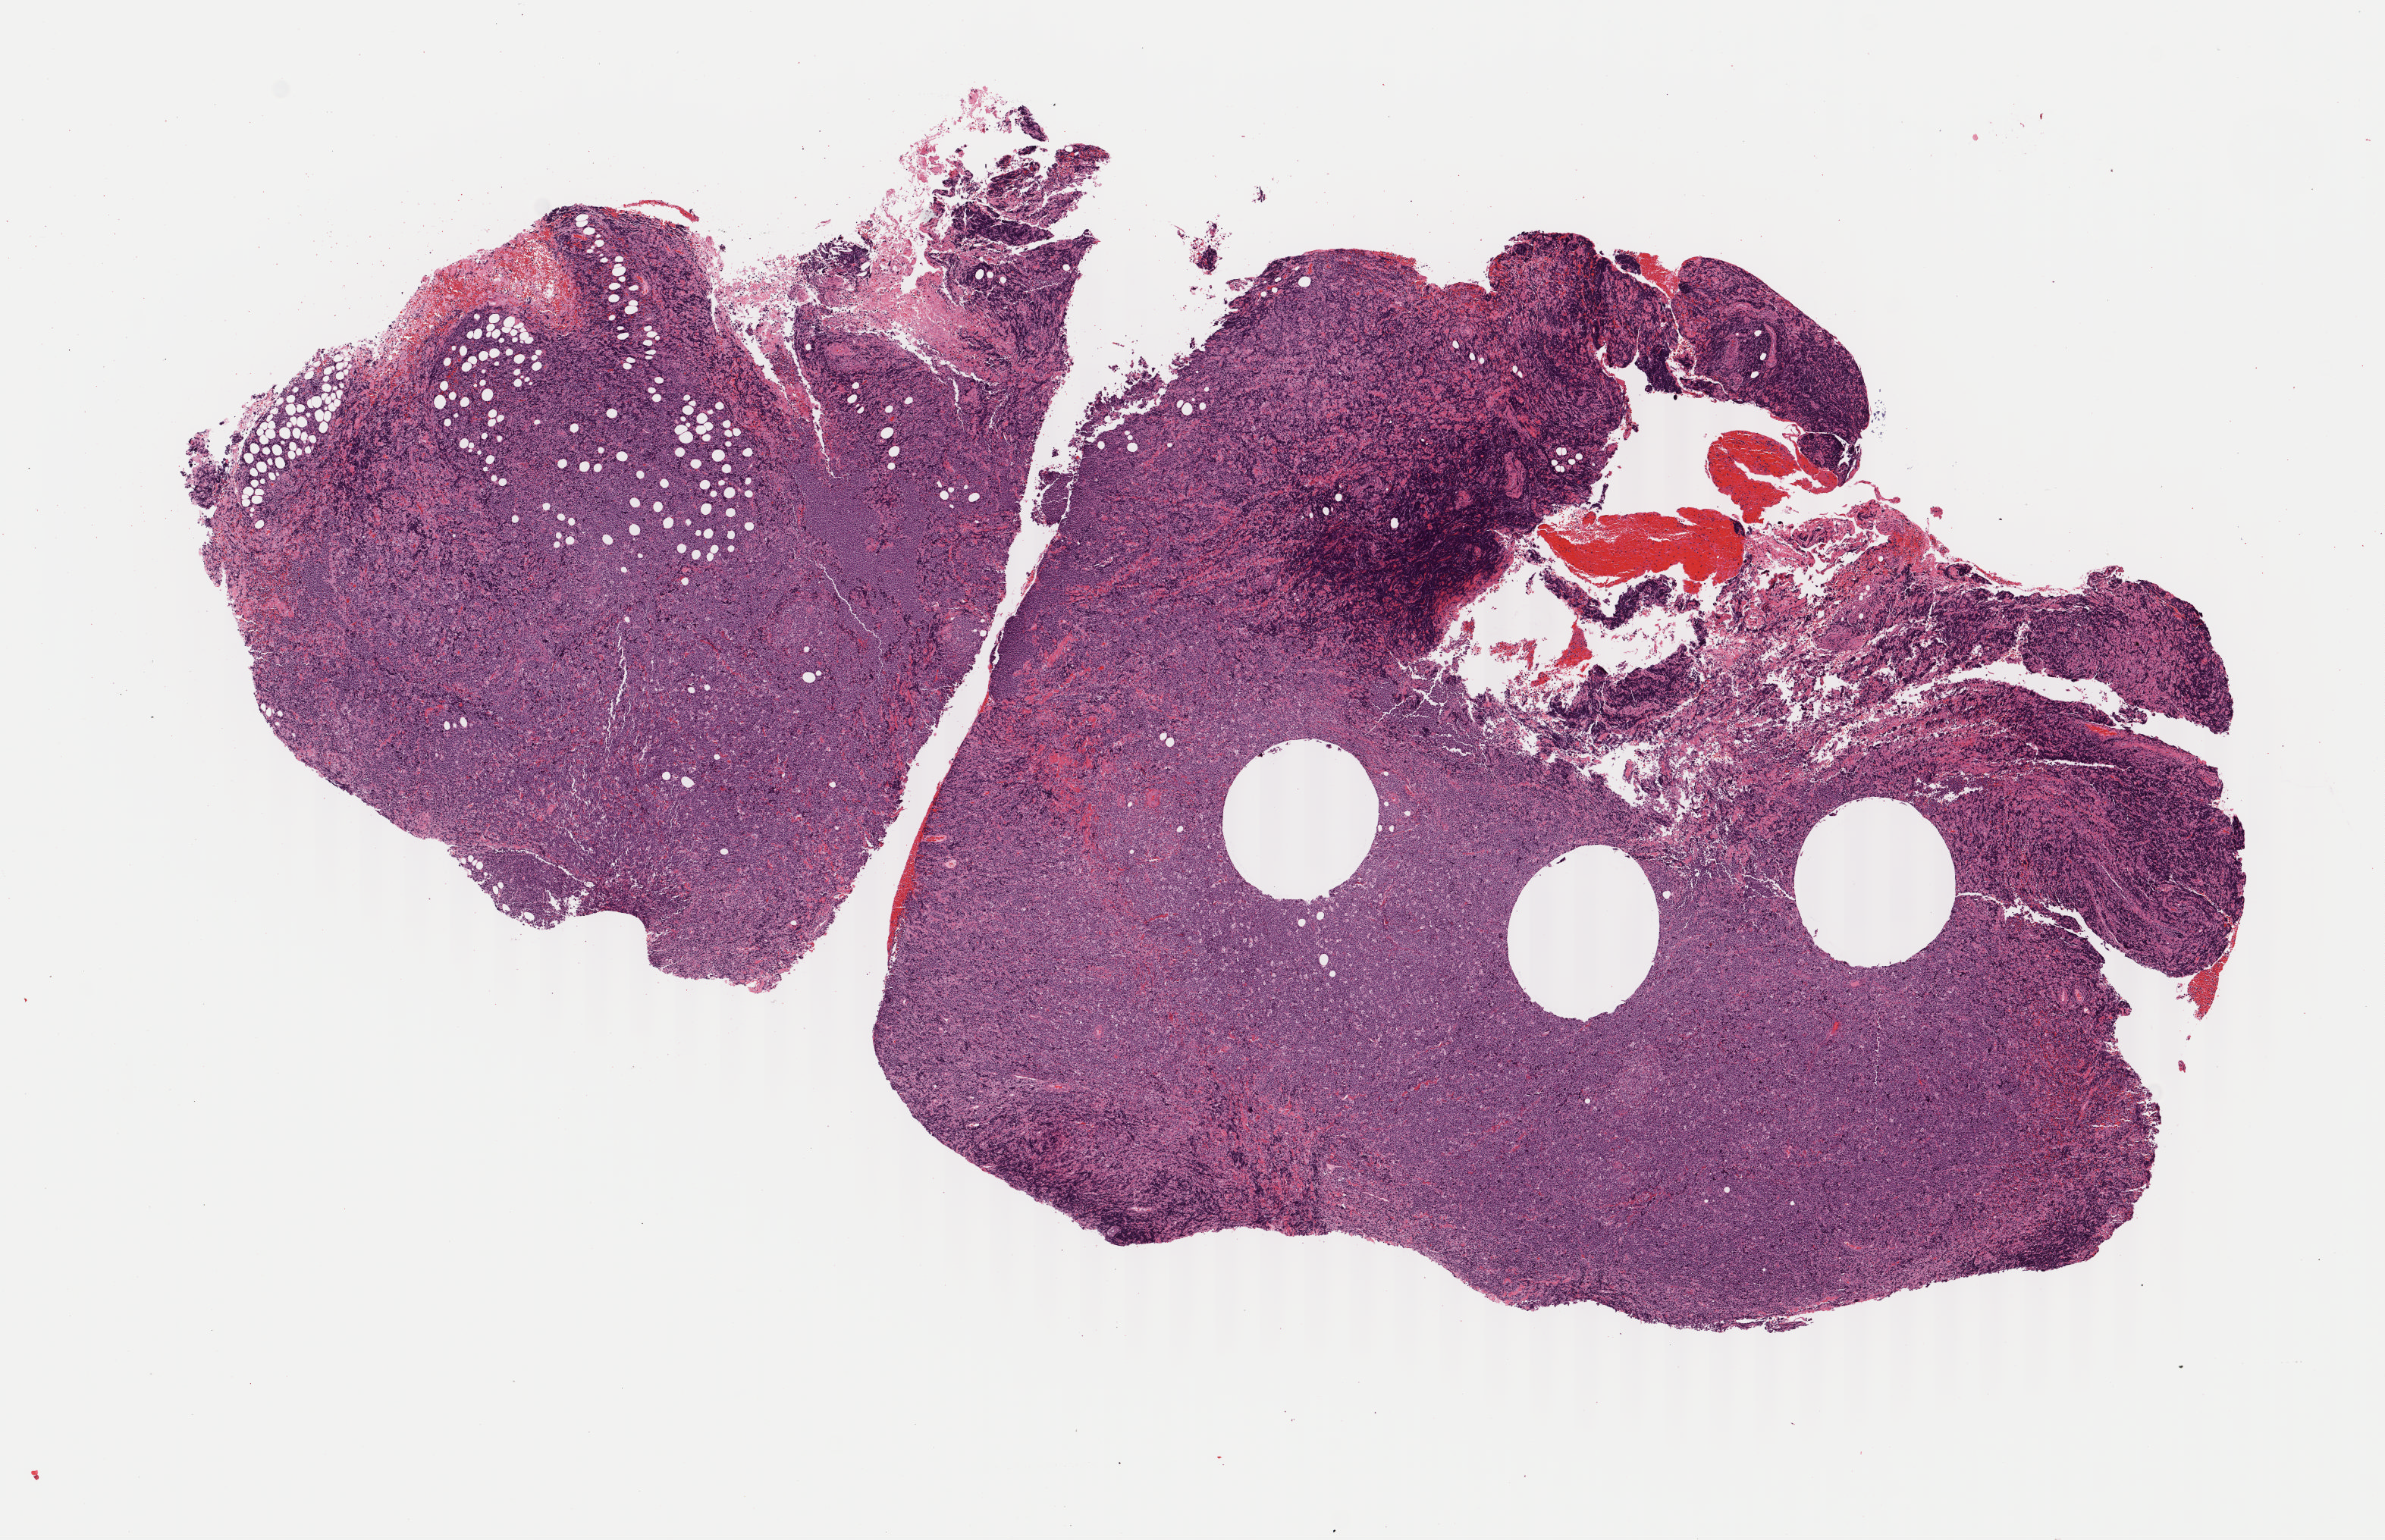
Haematoxylin and eosin whole-slide image — a low-resolution overview of the entire scanned area, about 12.5 x 8.1 mm; FFPE section; primary tumor; anatomic site: cranium. Patient: female, age at initial diagnosis 5 years. Pathologist review of this section (percent, as recorded): tumor cells 90%, tumor nuclei 90%, stromal cells 5%, necrosis 5%, normal cells 0%. Inflammatory infiltration, as recorded: lymphocyte infiltration 50%, monocyte infiltration 25%, neutrophil infiltration 5%.
• histologic diagnosis: Burkitt lymphoma, NOS
• Ann Arbor stage (patient): Stage IV